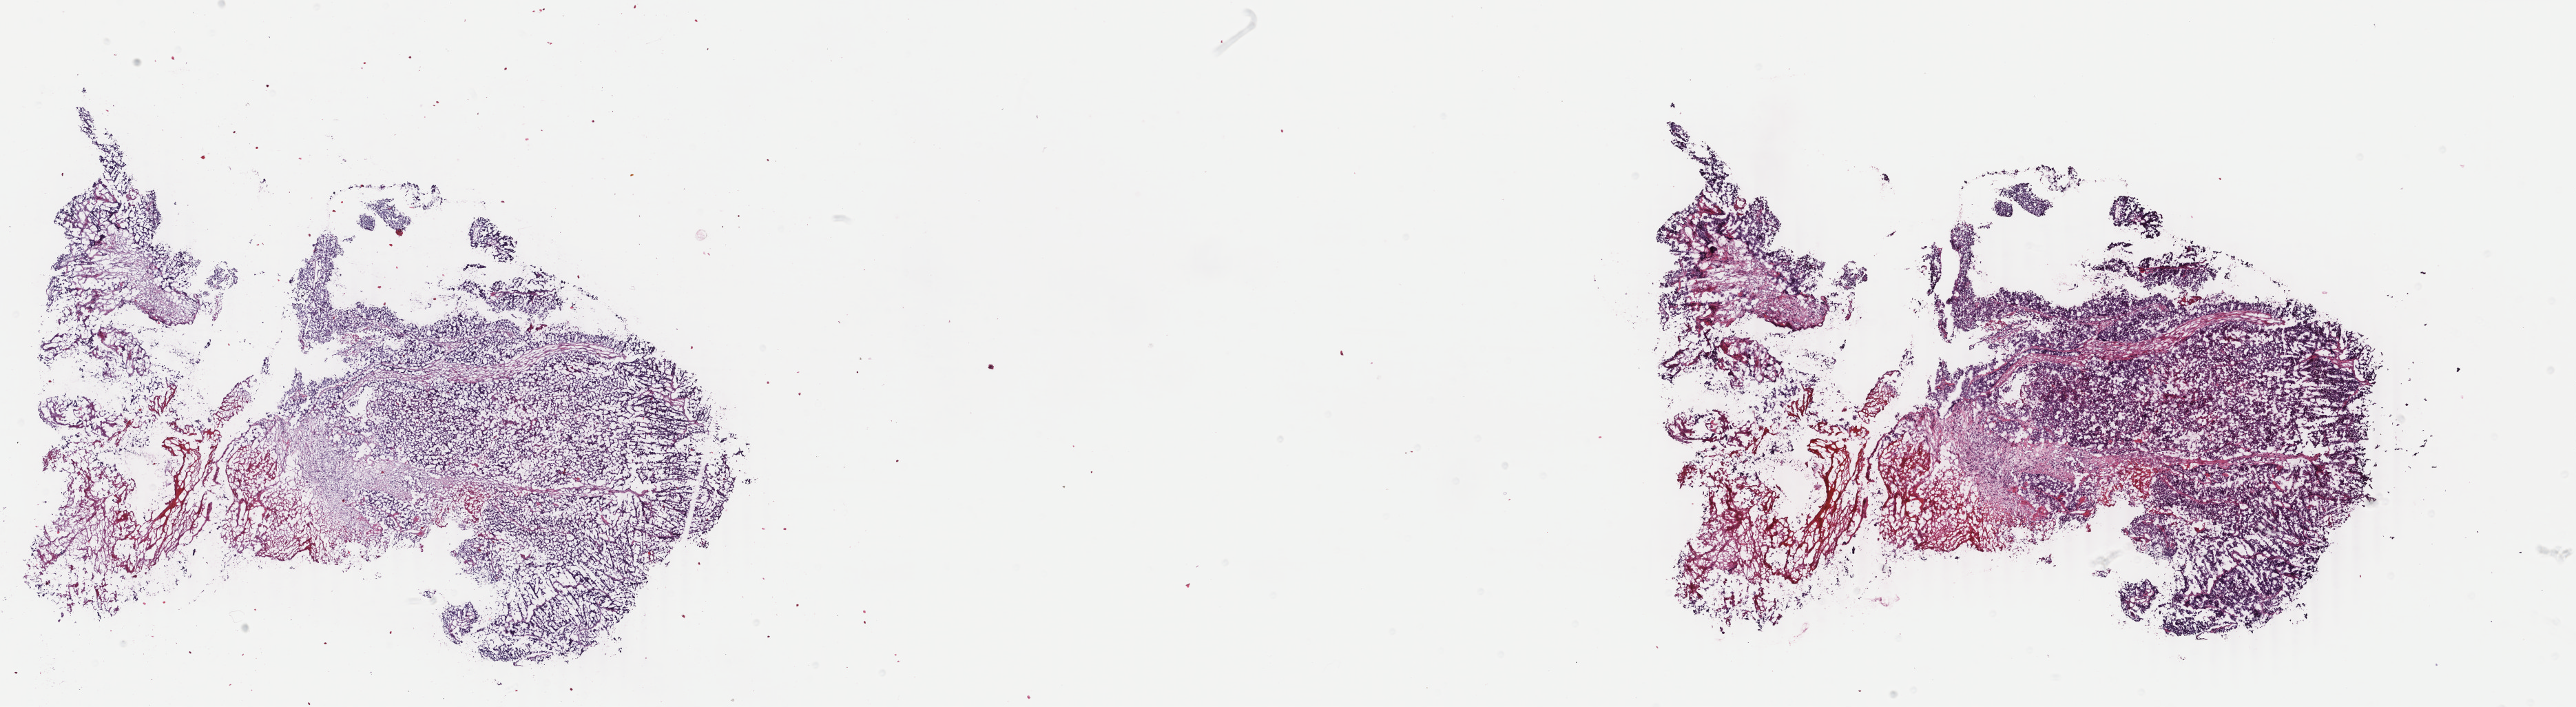
H&E whole-slide image — a low-resolution overview of the entire scanned area, about 29.7 x 8.2 mm (acquisition: 40x scan); frozen section; primary tumour sample from the uterus. Patient: female, age at initial diagnosis 51 years. Histologic grade: G2 (moderately differentiated). Slide review estimates, as recorded: tumour cells 60%, tumour nuclei 70%, normal cells 0%, stromal cells 20%, necrosis 20%. Inflammatory infiltration, as recorded: lymphocyte infiltration 0%, monocyte infiltration 0%, neutrophil infiltration 0%.
FIGO stage: IB. Histologic diagnosis: Endometrioid adenocarcinoma, NOS (endometrium).